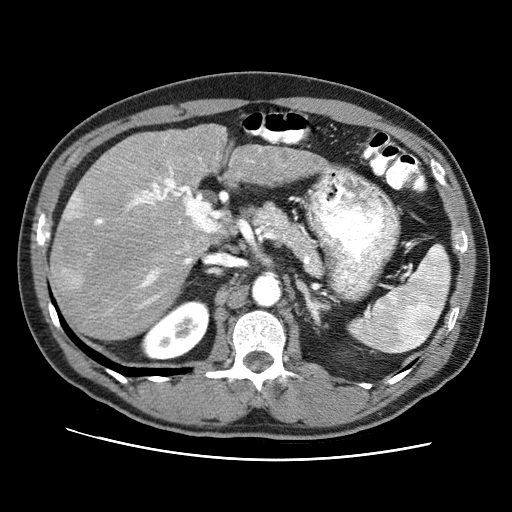
Contrast-enhanced abdominal CT (liver protocol), one axial slice. Position 45 of 71 along the scan axis. Reconstruction kernel STANDARD. 120 kVp. Soft-tissue window (W 400 / L 40 HU). 2.5 mm slice thickness. 512 × 512 image matrix, field of view 360 × 360 mm. Case-level facts recorded for this patient, not image findings: diagnosis: hepatocellular carcinoma (patient treated with transarterial chemoembolisation; whether this scan precedes or follows treatment is not stated here); TNM stage (as recorded): Stage-II; Child-Pugh class: A; tumour size: 4.6 cm.
Annotated regions visible in this slice (semi-automatic segmentation, software-assisted and operator-edited):
- liver parenchyma outside the tumour (the mass and vessels are separate outlines, so this box may not span the whole liver): bounding box <50,124,329,340> (left, top, right, bottom; pixels)
- mass: <50,192,91,291>
- liver vessels: <95,157,201,304>